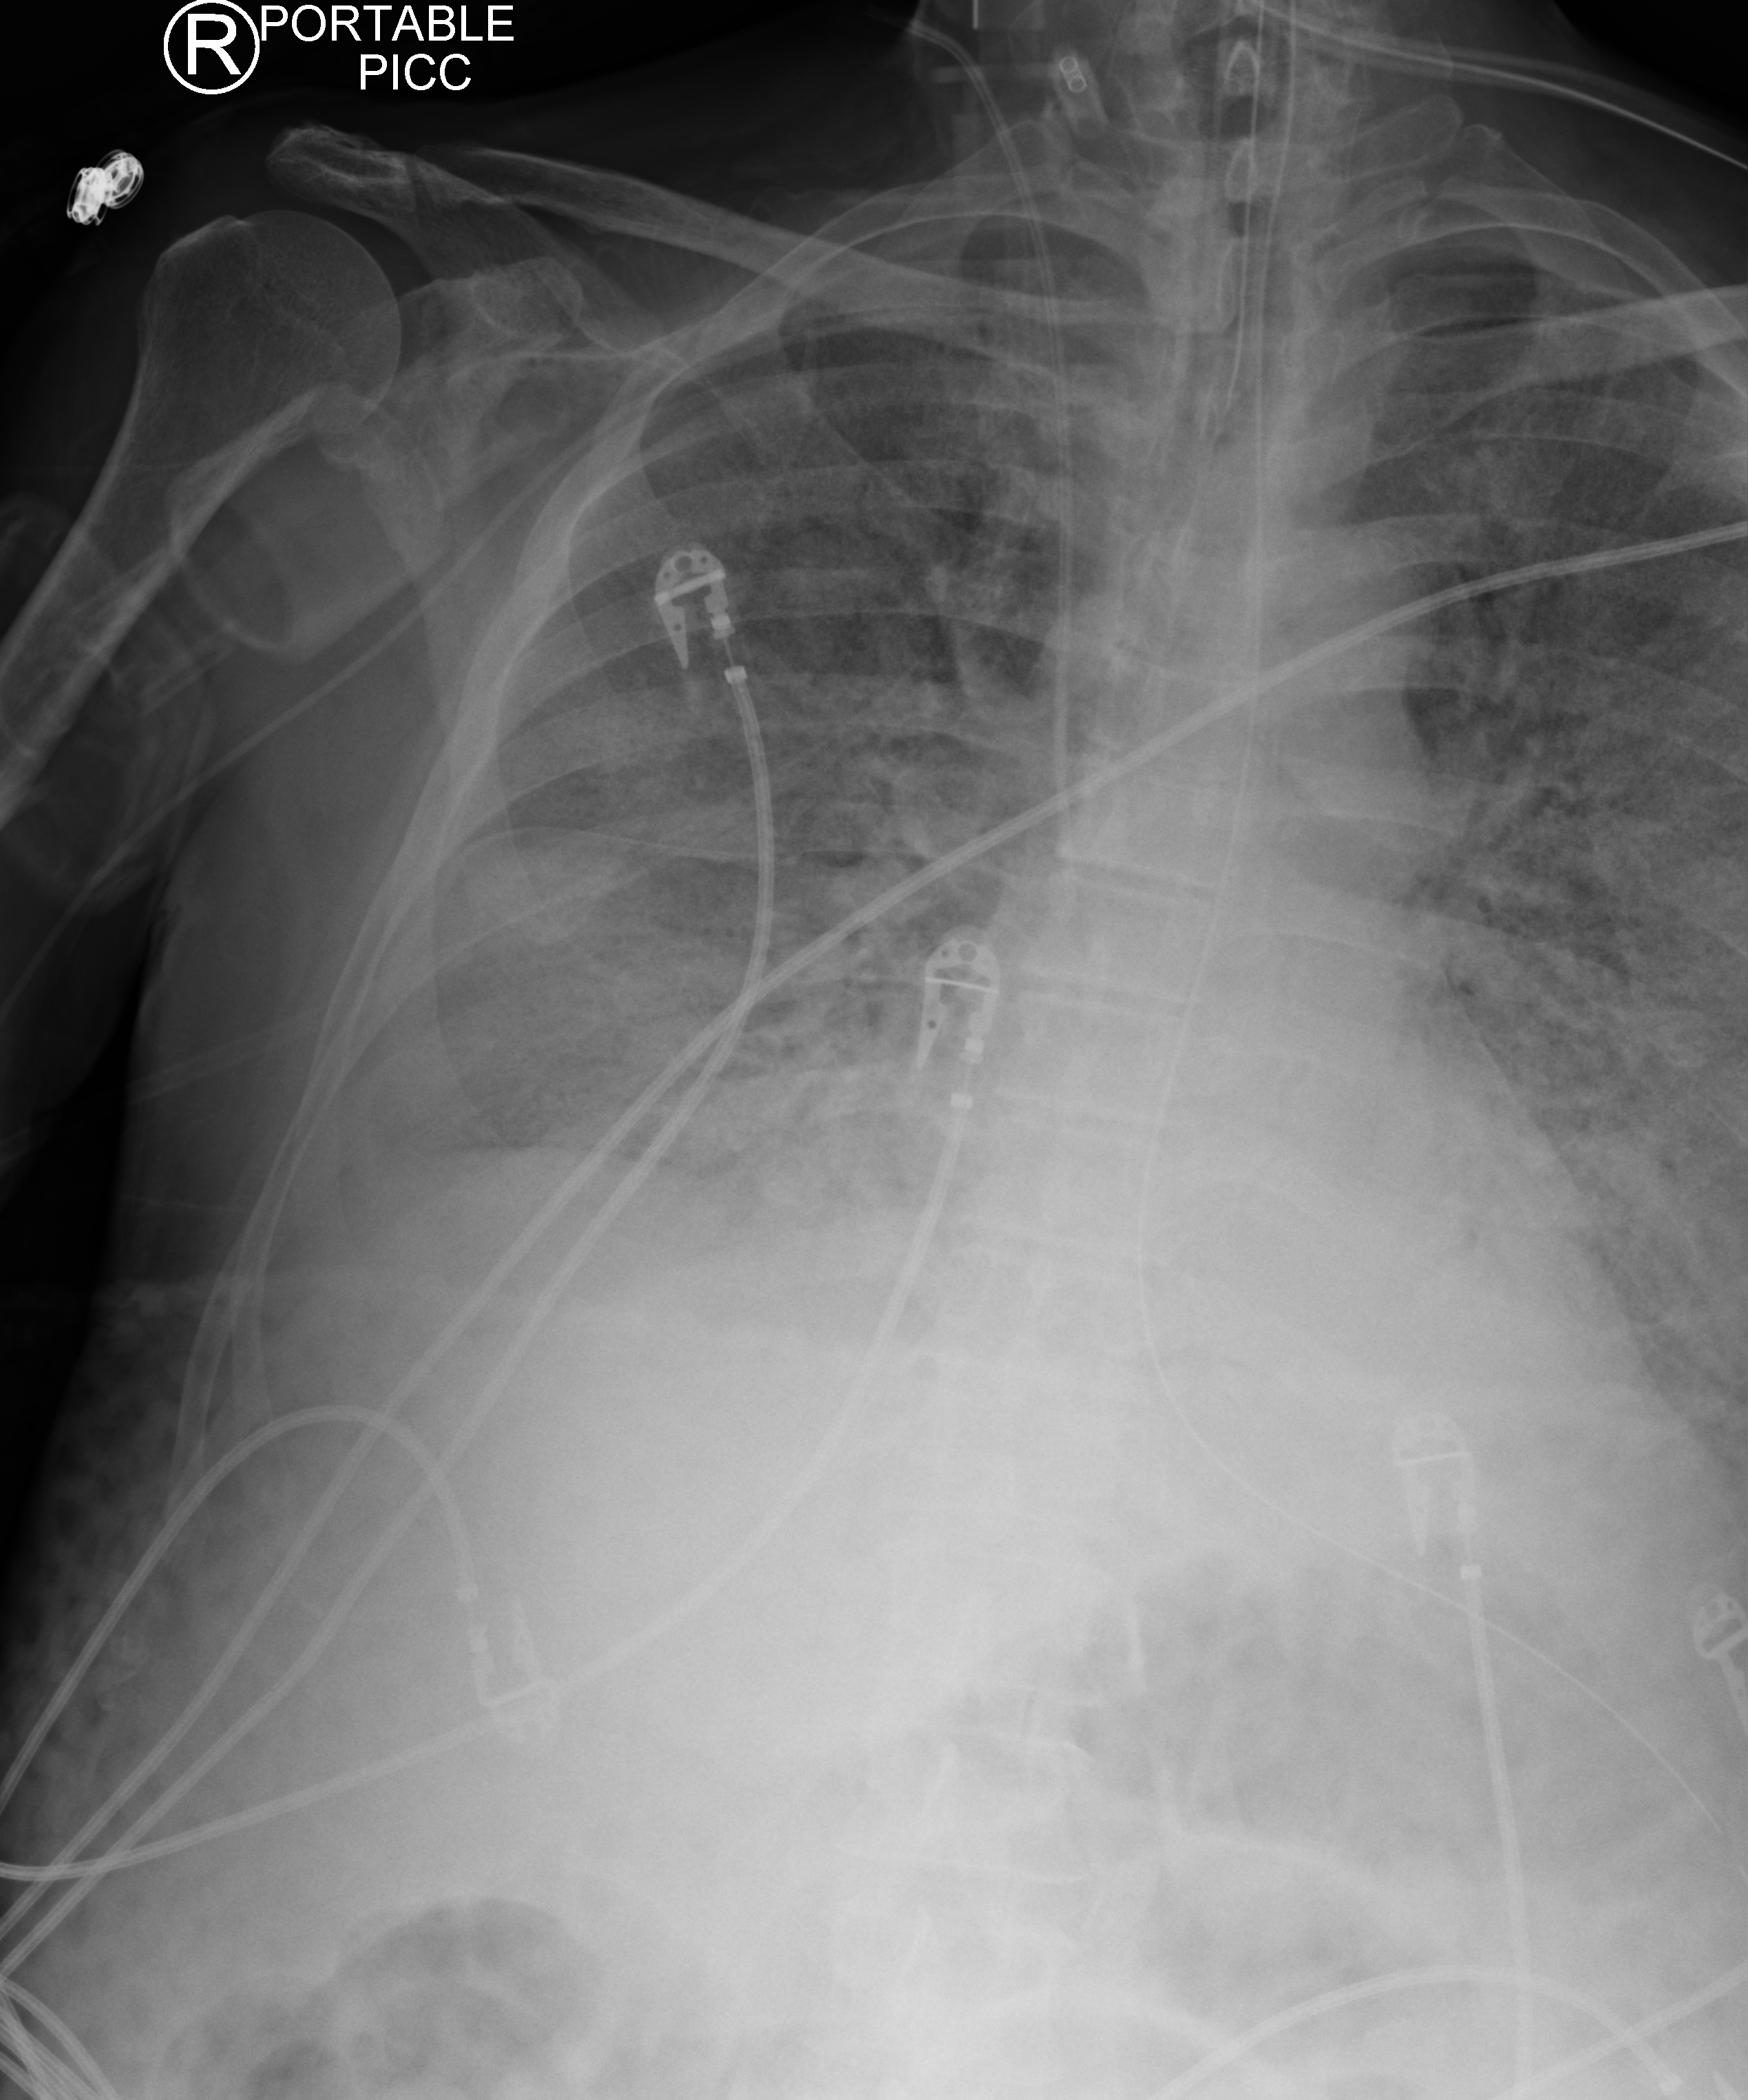
Portable chest radiograph, anteroposterior (AP) projection. Patient hospitalised with COVID-19; male, aged 60–74 years.
Hospital-stay facts (about this admission, not read from this image; timing relative to this image not recorded): diabetes (admission record): yes.